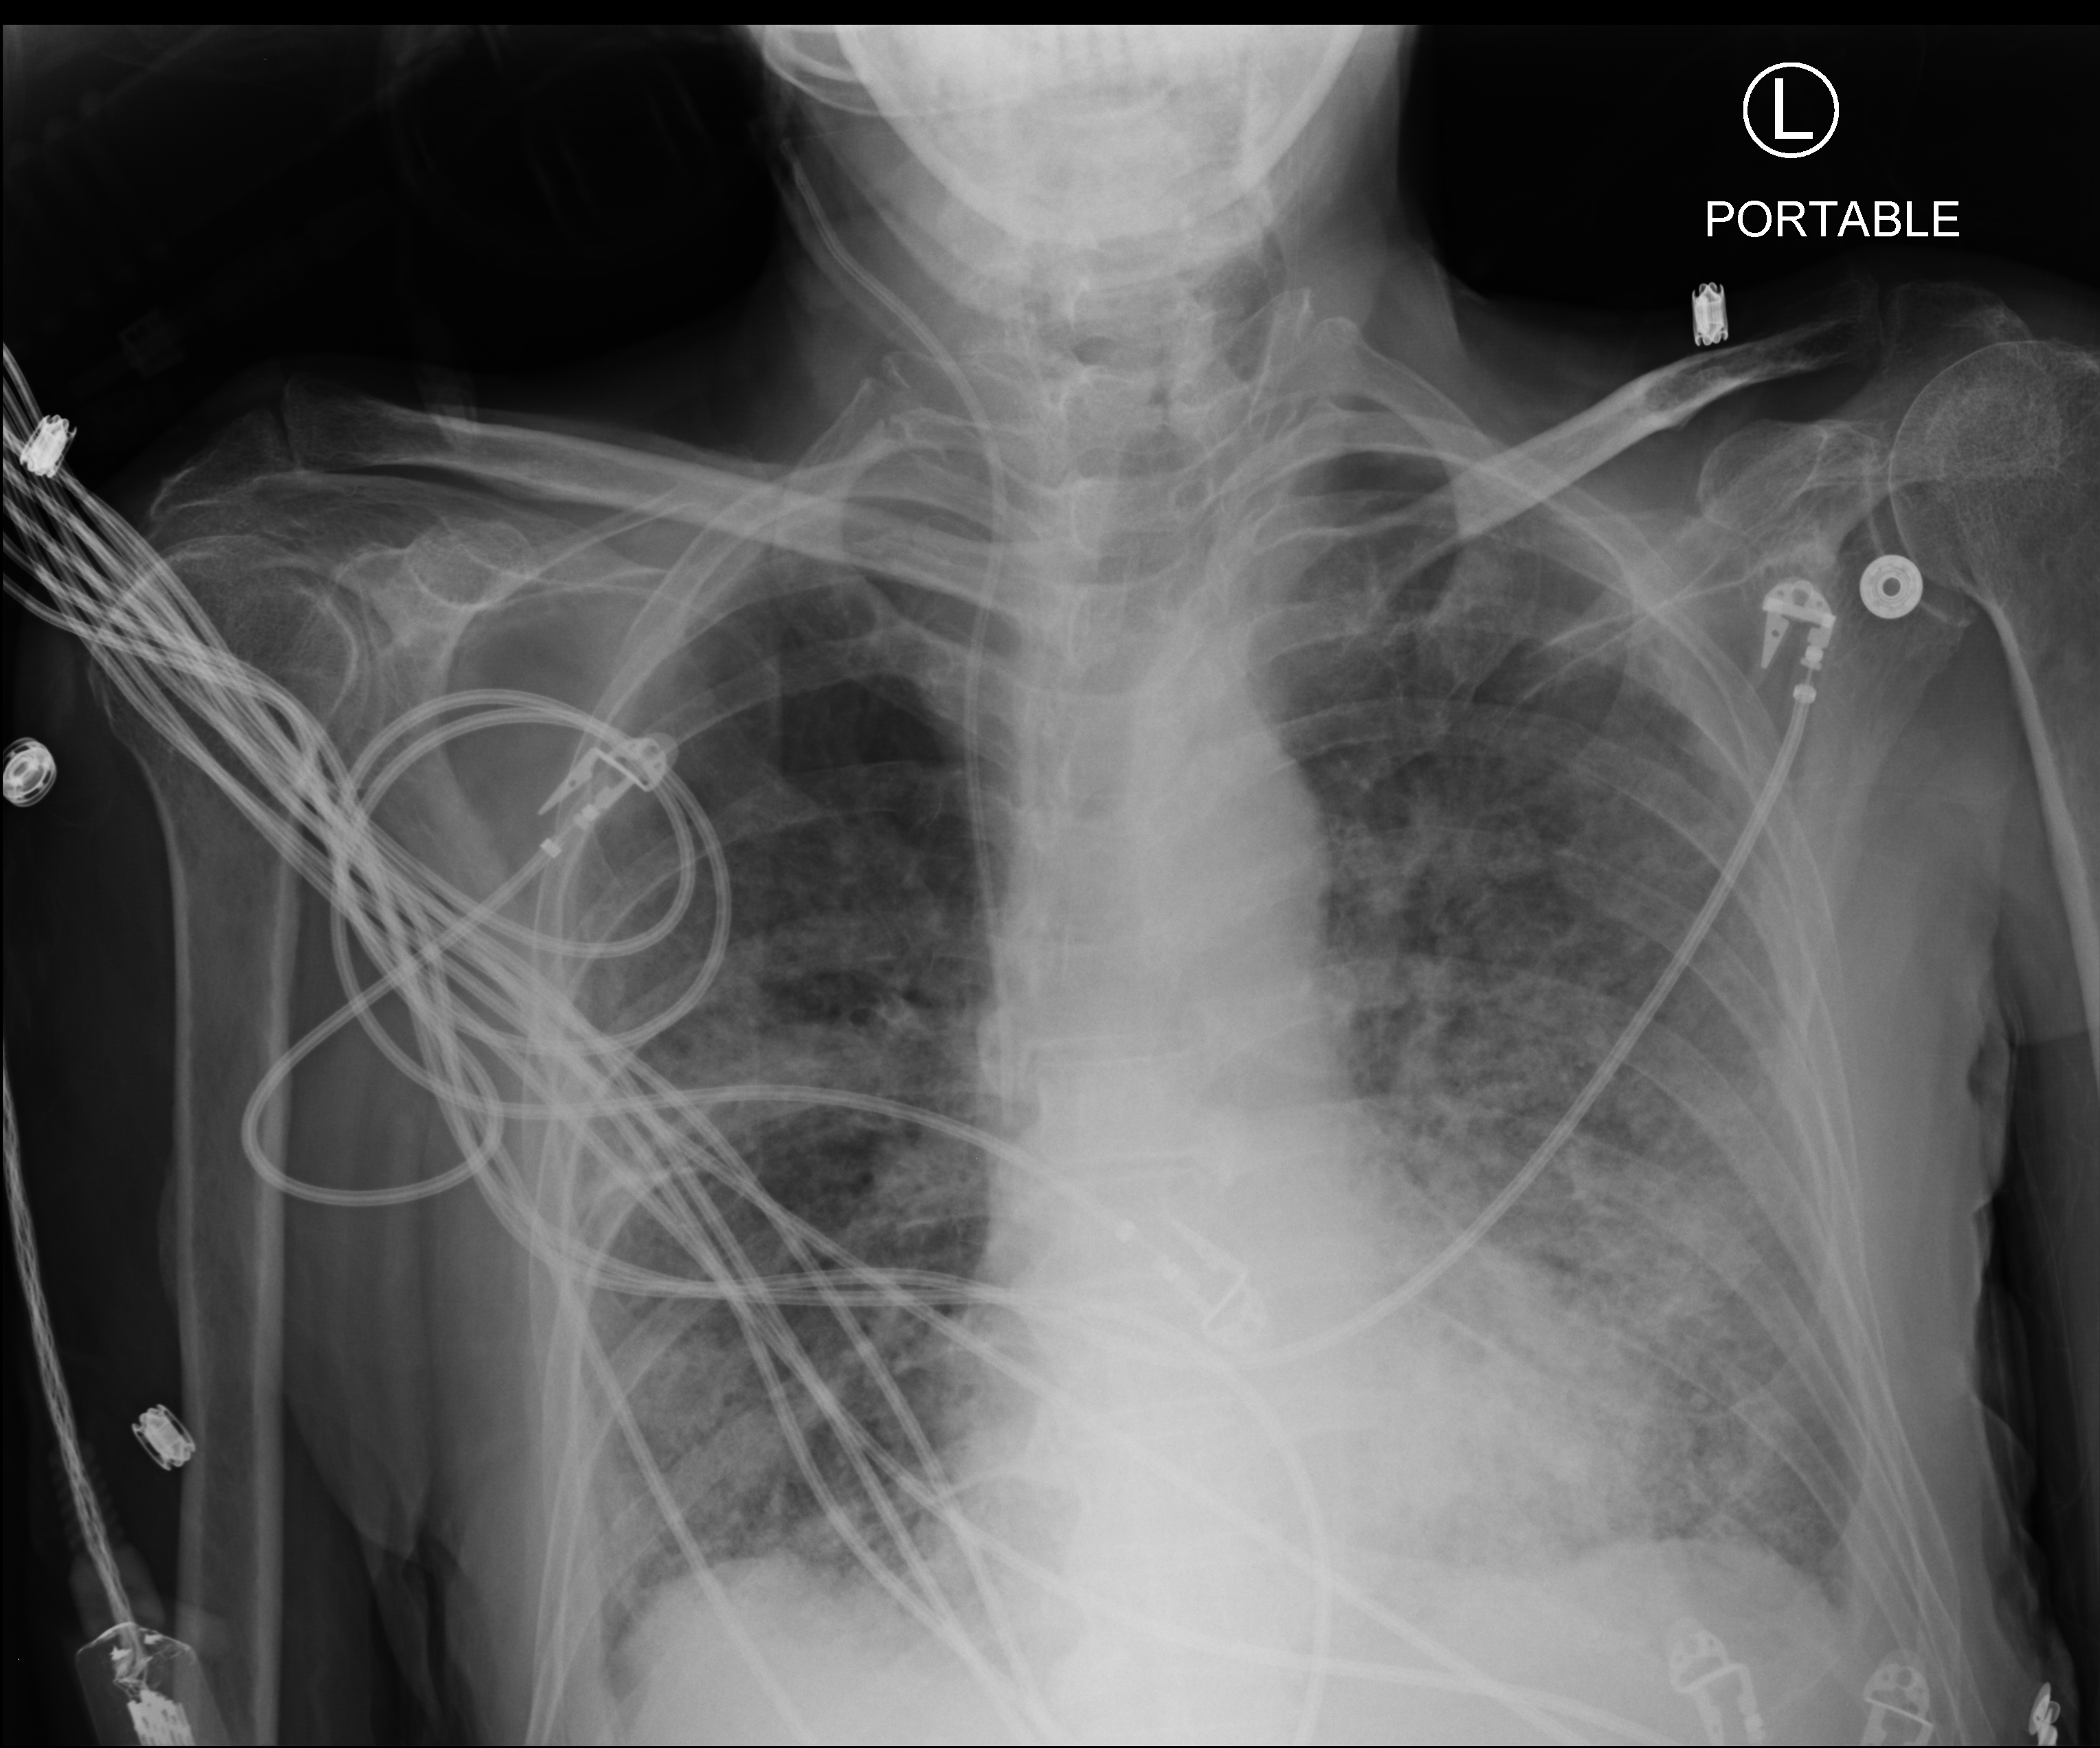
Portable chest radiograph; anteroposterior (AP) projection. Patient hospitalised with COVID-19; male, aged 60–74 years.
Hospital-stay facts (about this admission, not read from this image; timing relative to this image not recorded): smoking status (admission record): current.